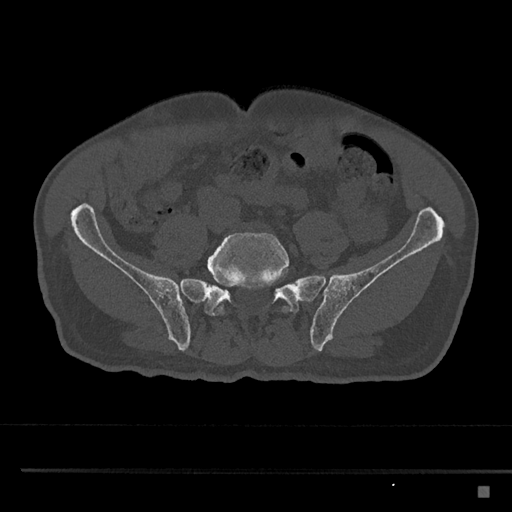
CT including the spine, one axial slice. Position 560 of 797 along the scan axis. Reconstruction kernel Br40s/3. 120 kVp. Bone window (W 1800 / L 400 HU). 0.5 mm slice thickness. 512 × 512 image matrix, field of view 391 × 391 mm. Male patient, age 59 years. From the clinical record (not read from this slice): primary cancer: prostate.
Structures marked on this image (semi-automatic segmentation, software-assisted and operator-edited):
- L5 vertebra: bounding box <207,232,291,316> (left, top, right, bottom; pixels)